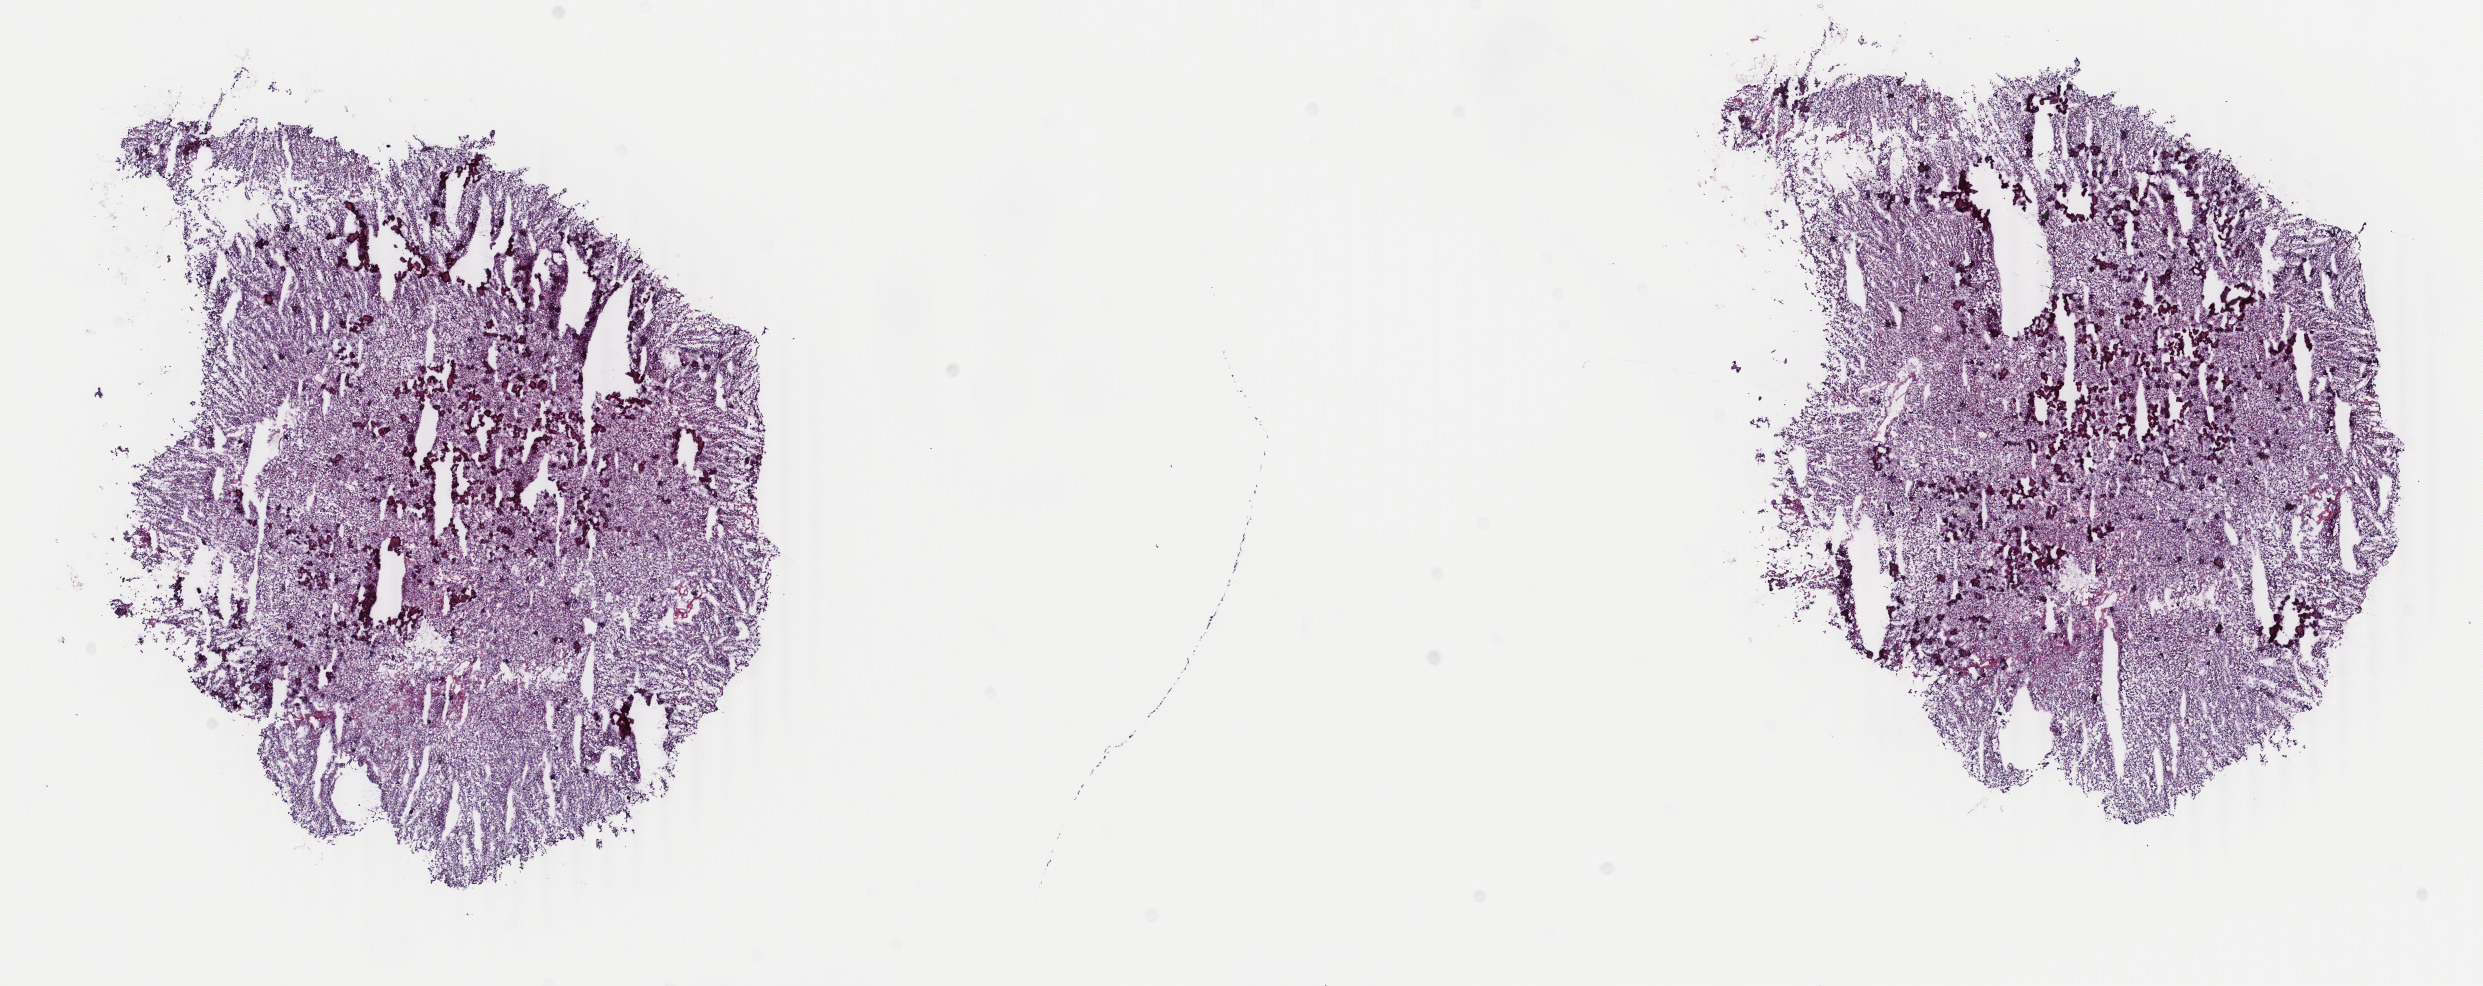
Whole-slide histology image, H&E-stained — a low-resolution overview of the entire scanned area, about 19.8 x 7.8 mm (from a 40x scan); frozen section from the top of the tissue portion; primary tumour sample from the brain. Patient: female, age at initial diagnosis 51 years. Histologic grade: G3 (poorly differentiated). Slide review estimates, as recorded: tumour cells 80%, tumour nuclei 90%, normal cells 5%, stromal cells 15%, necrosis 0%. Inflammatory infiltration, as recorded: lymphocyte infiltration 0%, monocyte infiltration 0%, neutrophil infiltration 0%.
Diagnosis: Oligodendroglioma, anaplastic (cerebrum). Laterality: left.